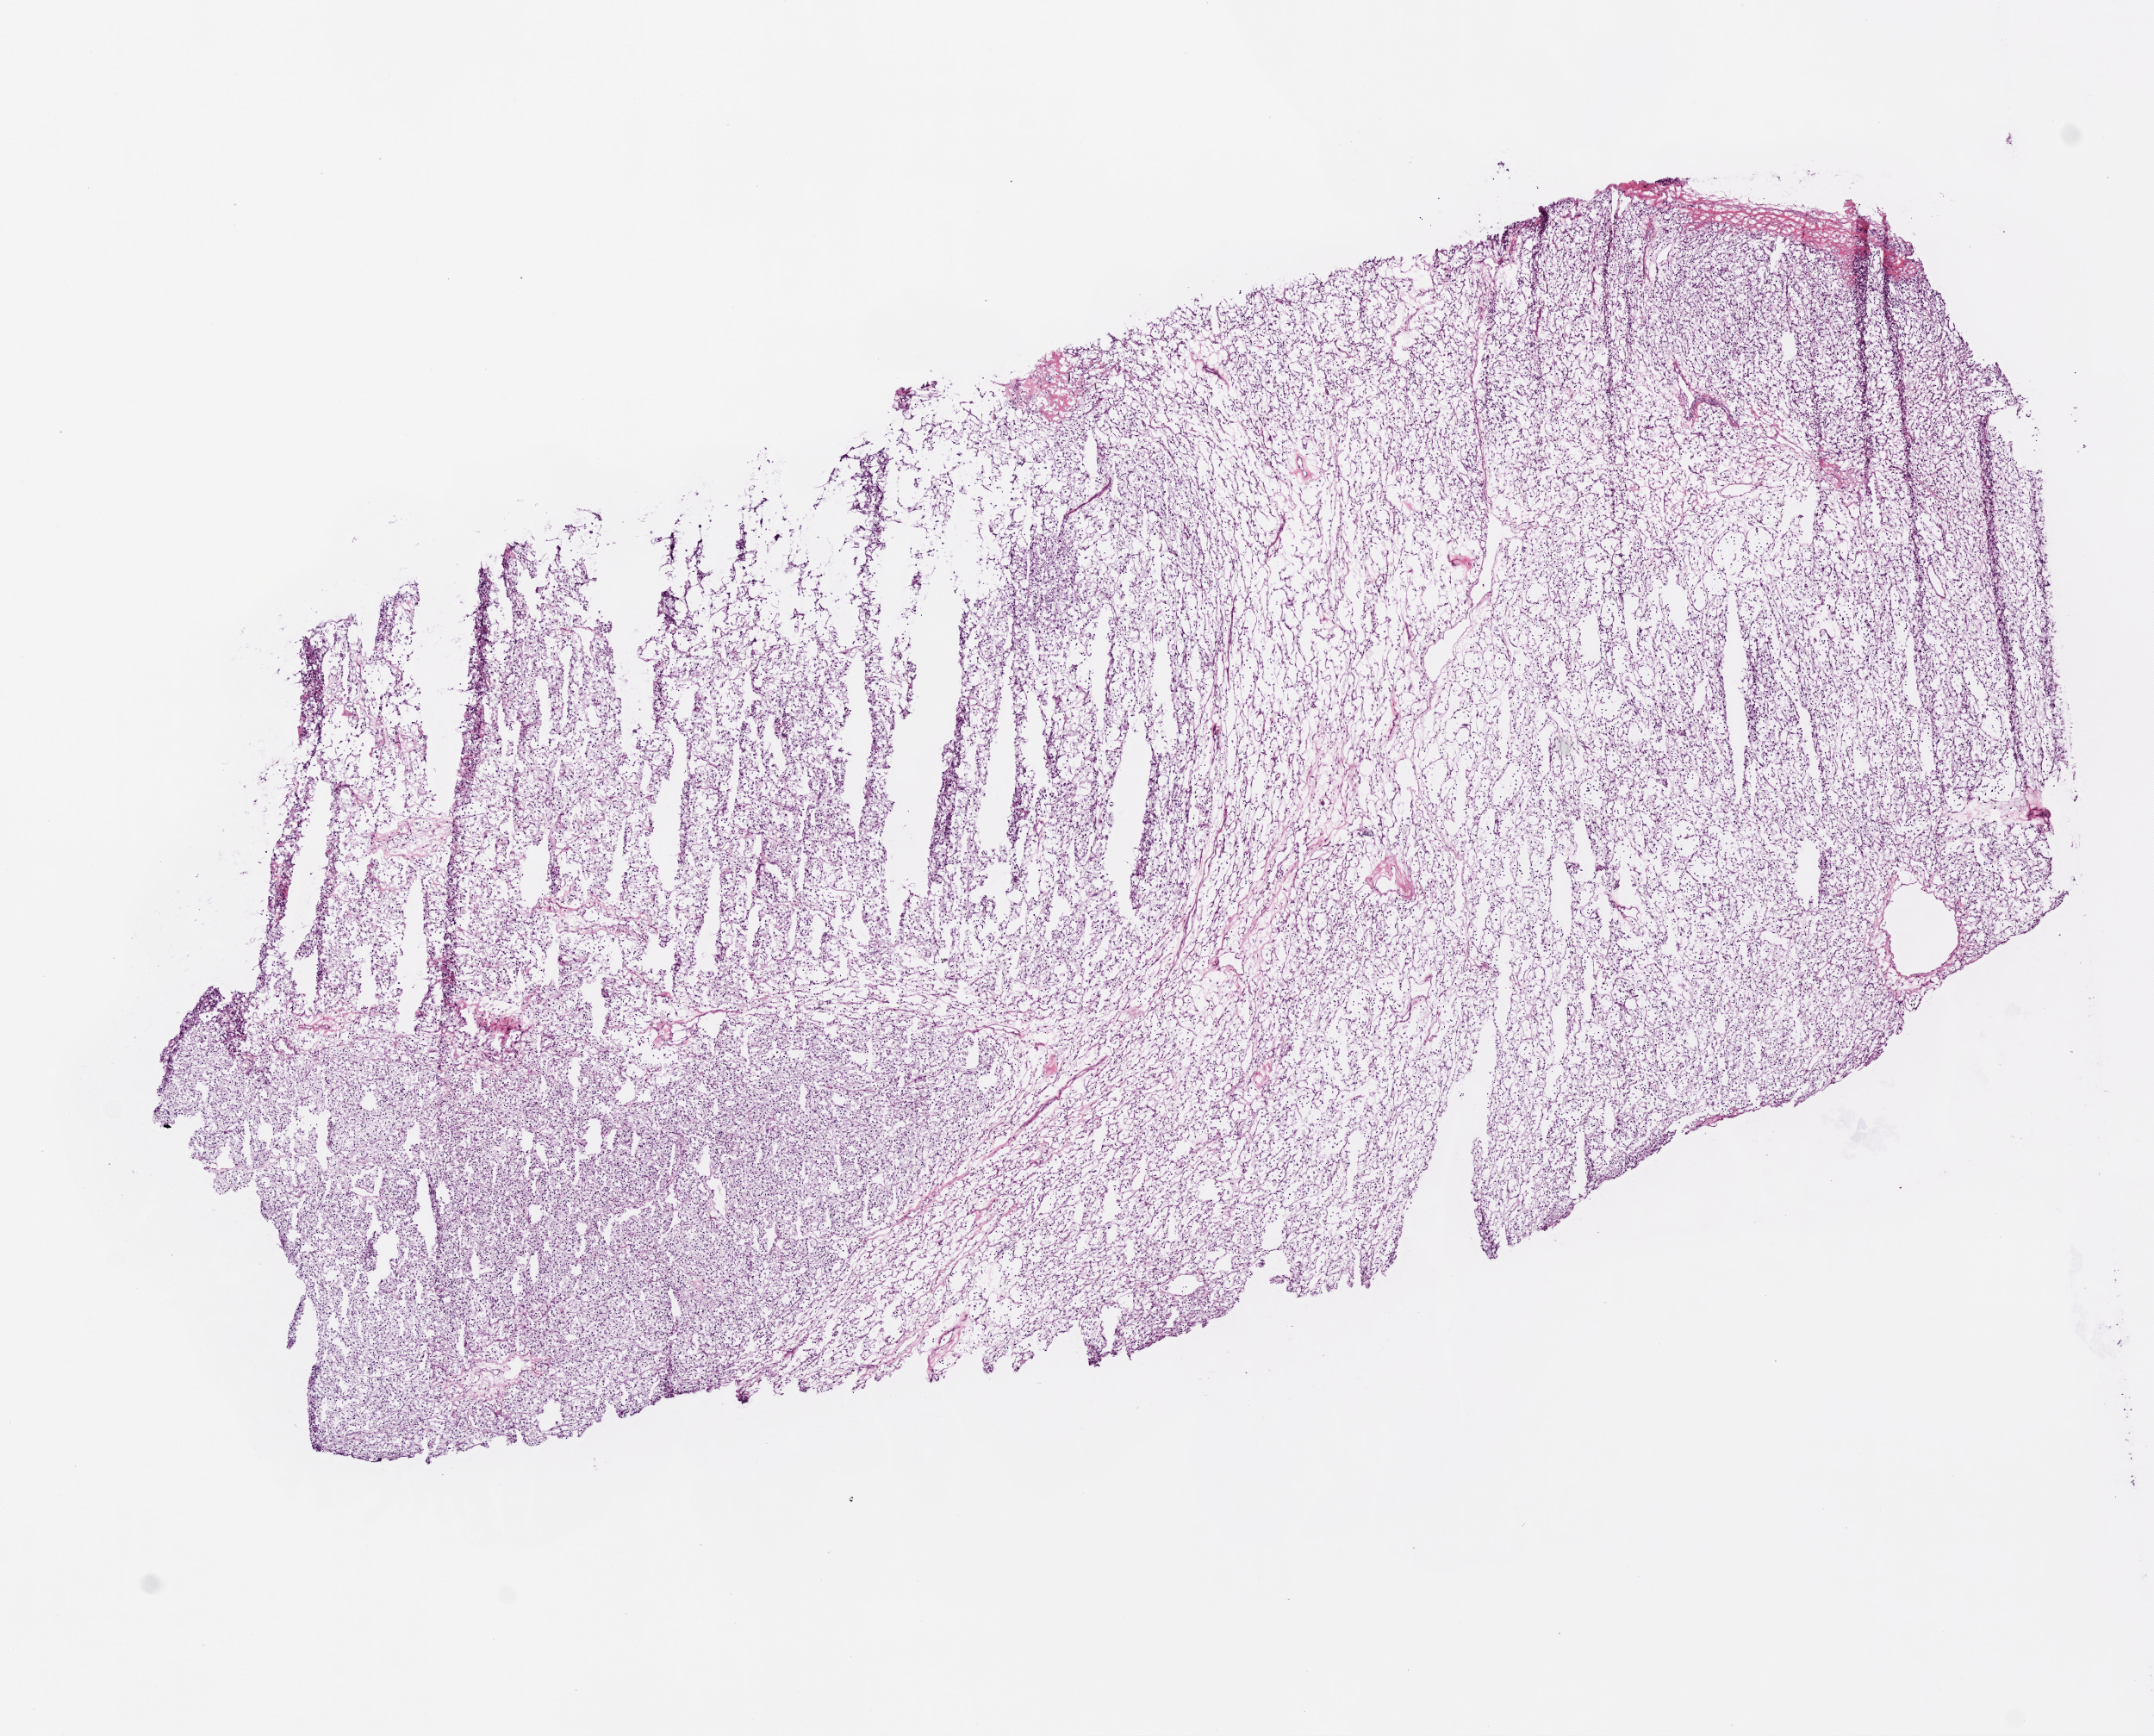
Hematoxylin and eosin (H&E) stained whole-slide image, a low-resolution overview of the entire scanned area, about 10.0 x 8.1 mm. Frozen section from the top of the tissue portion. Kidney, primary tumour sample. Female, age 73 years at initial diagnosis. Histologic grade: G3 (poorly differentiated). Slide review estimates, as recorded: tumour cells 95%, tumour nuclei 85%, normal cells 0%, stromal cells 5%, necrosis 0%.
AJCC pathologic stage: IV. Pathologic diagnosis: Clear cell adenocarcinoma, NOS.